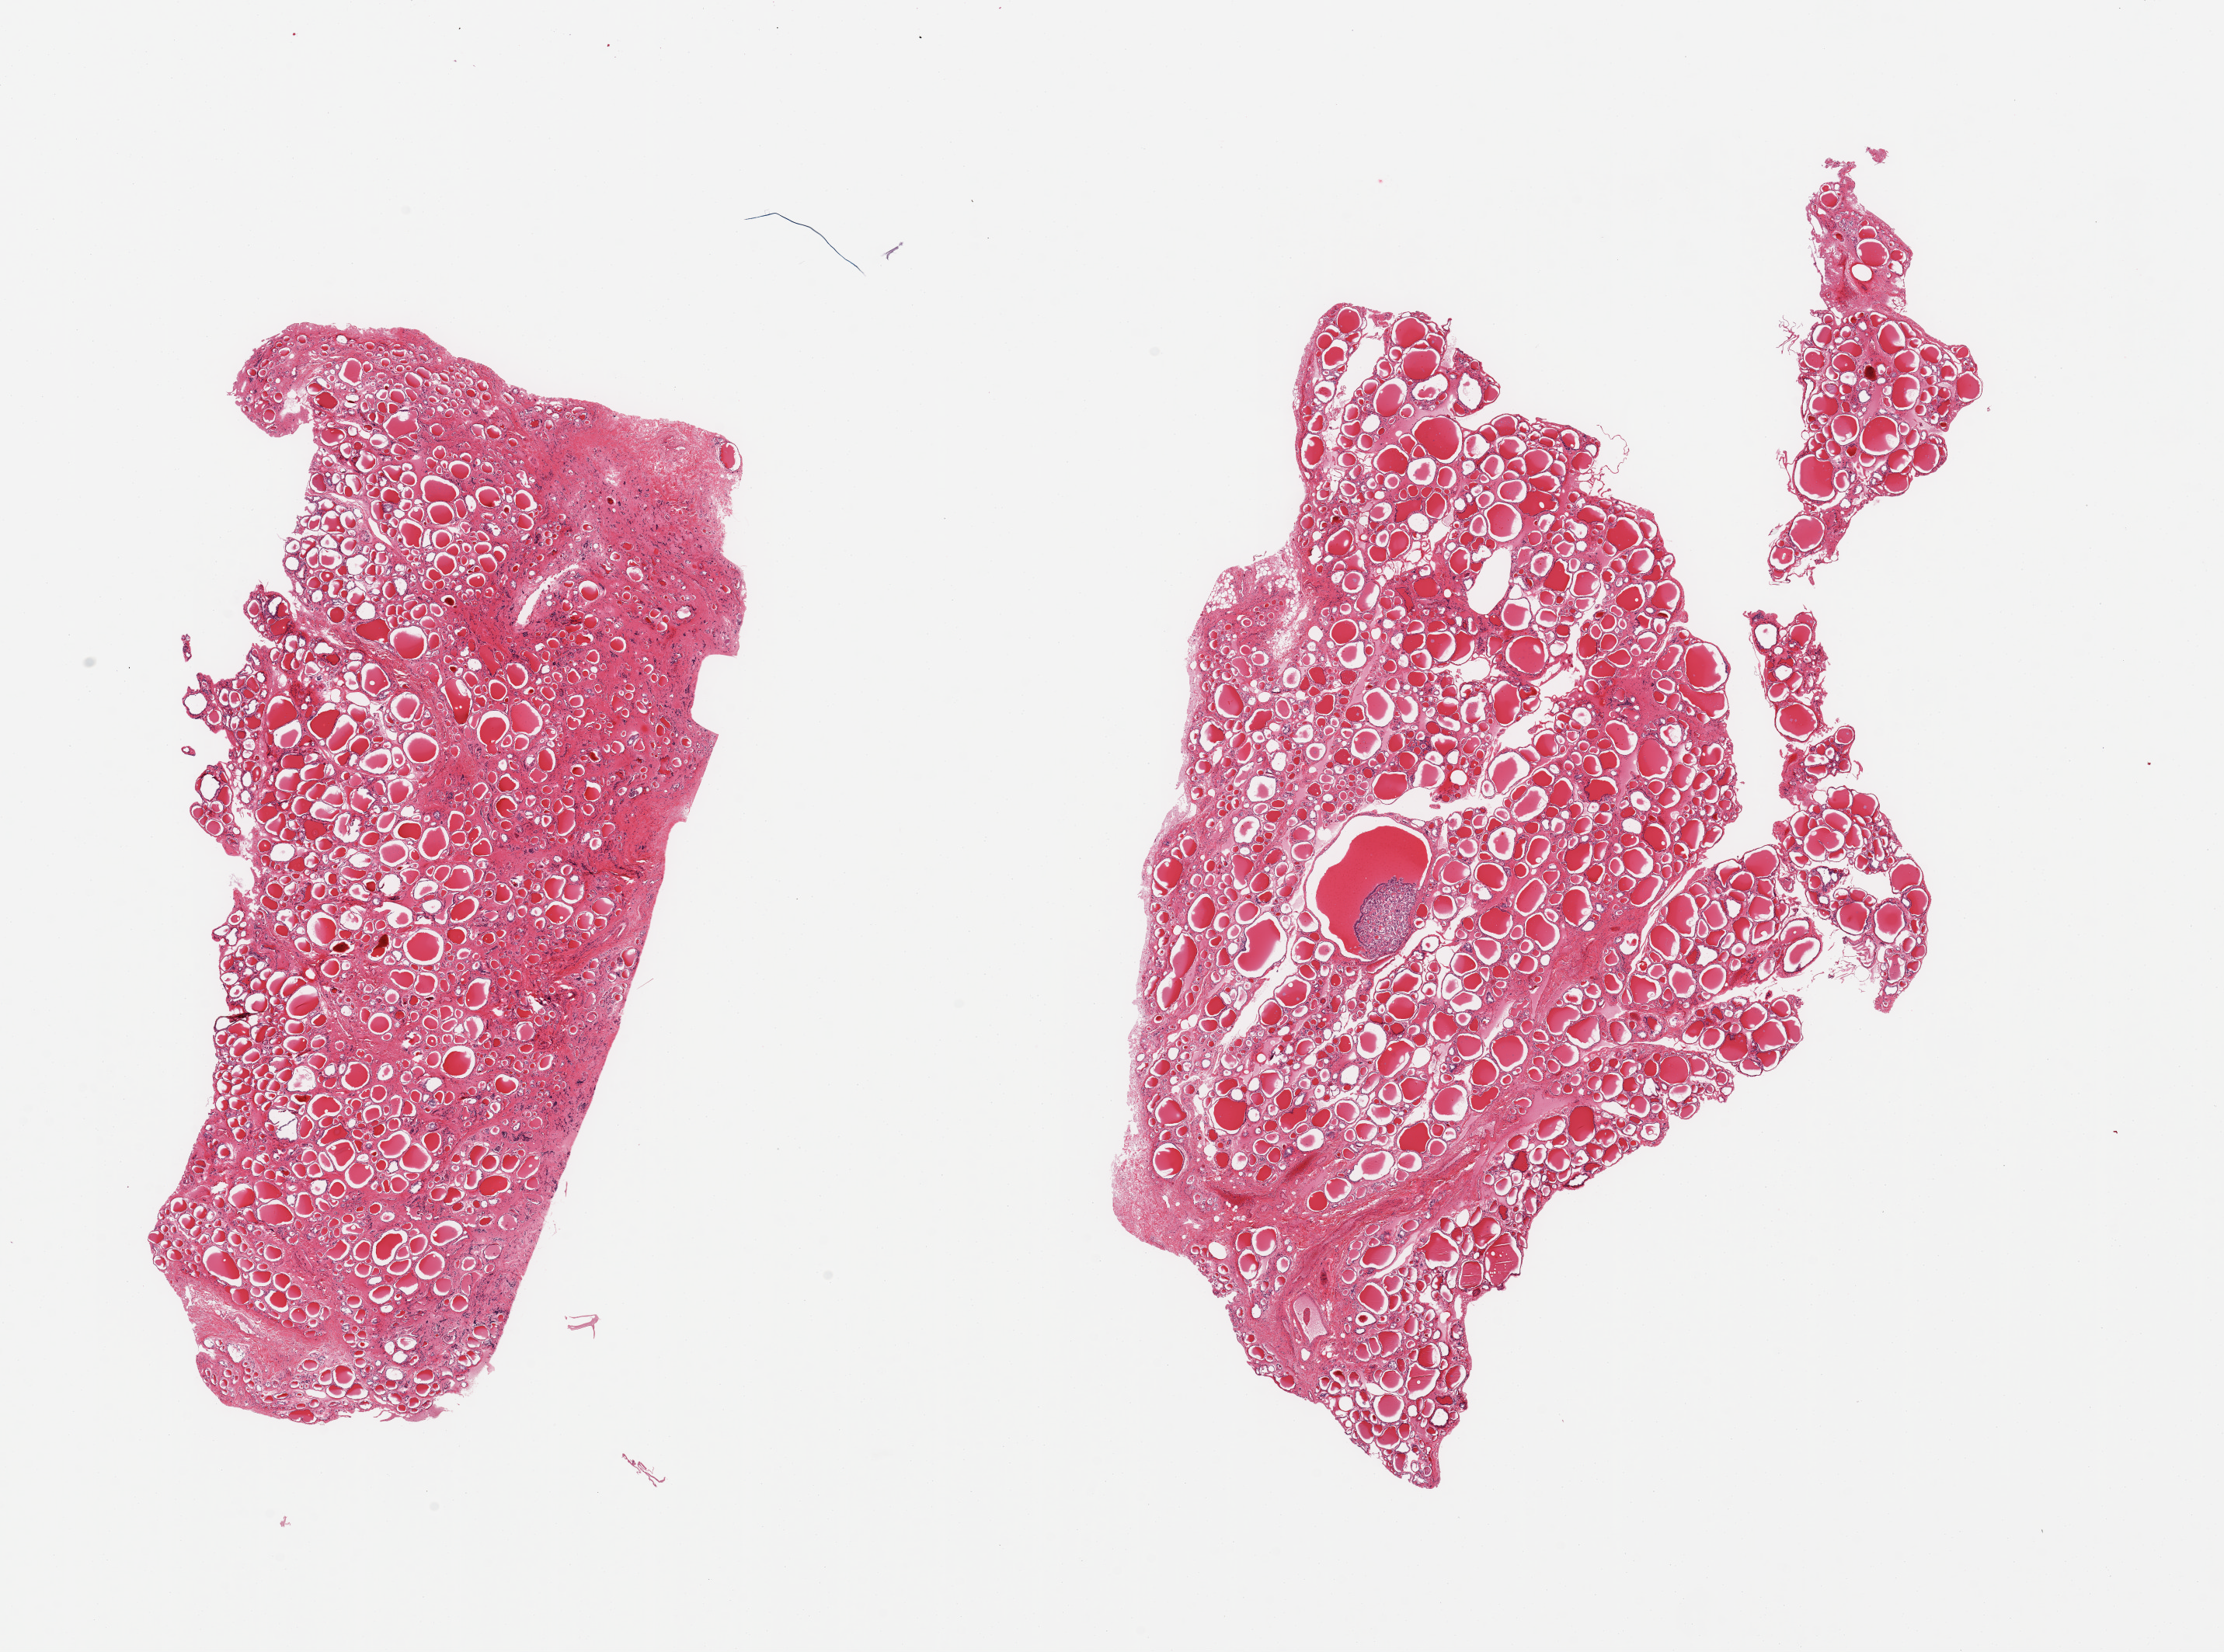
Digitized haematoxylin and eosin-stained section — a low-resolution overview of the entire scanned area, about 22.6 x 16.8 mm. PAXgene-fixed, paraffin-embedded tissue. Target tissue: thyroid. Tissue donor sample. Male donor.
Reviewer comment on this tissue sample: 2 pieces, mild goitrous changes.